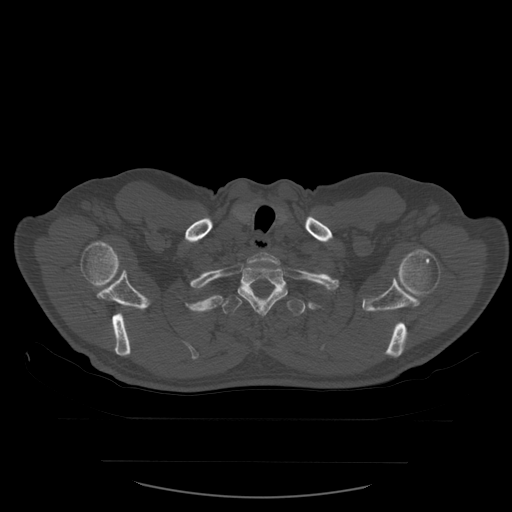
CT including the spine, one axial slice; position 472 of 590 along the scan axis; bone window (W 1800 / L 400 HU); 512 × 512 image matrix, field of view 479 × 479 mm. Patient age 71 years. Case-level facts recorded for this patient, not image findings: primary cancer: lung; vertebrae with lytic lesions (as recorded): T1, T2, L5, S1.
Annotated regions visible in this slice (semi-automatically segmented with operator editing):
- T1 vertebra: bounding box (x1, y1, x2, y2) in pixels: (248, 252, 280, 268)
- T2 vertebra: (238, 263, 288, 315)
- T3 vertebra: (221, 295, 306, 345)